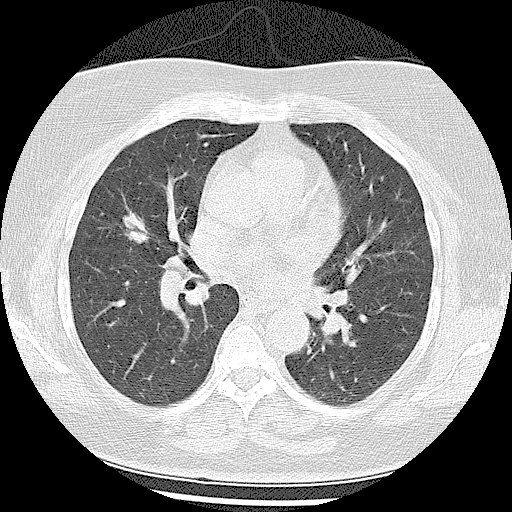
Axial slice from a low-dose chest CT screening exam; first (baseline) screen; lung window (W 1500 / L -600 HU); 2.5 mm slice thickness; lung (sharp) reconstruction kernel (LUNG); slice 50 of 102 in the series. Female, age 57 years at enrolment. Former smoker at enrolment.
Lesion marked by an expert reader, bounding box [x1, y1, x2, y2] px = [104, 203, 168, 259]. The screening reader recorded 4 non-calcified nodules or masses ≥4 mm on this exam (right middle lobe, right lower lobe, left lower lobe, left lower lobe); which of them this box marks is not recorded. Later outcome: lung cancer diagnosed 87 days after this screen — adenocarcinoma, NOS, right middle lobe, well differentiated (G1), stage IA (AJCC 6th edition), 21 mm at pathology.